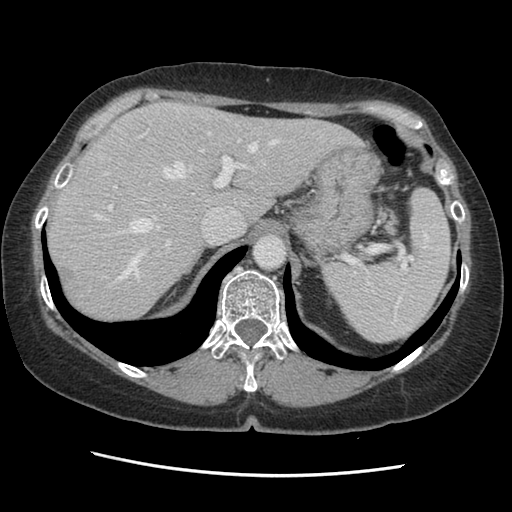
Contrast-enhanced abdominal CT, one axial slice; position 101 of 141 along the scan axis; soft-tissue window (W 400 / L 40 HU); 2.5 mm slice thickness; 512 × 512 image matrix, field of view 330 × 330 mm. Female patient, age 61 years. Case-level facts recorded for this patient, not image findings: diagnosis: colorectal cancer liver metastases, imaged before liver resection; multiple liver metastases: no; largest metastasis: 2.4 cm; chemotherapy before resection: no.
Structures marked on this image (manually delineated by an expert):
- hepatic veins: bounding box <94,117,278,282> (left, top, right, bottom; pixels)
- liver: <48,103,356,323>
- planned liver remnant (the part of the liver to remain after resection): <48,103,356,323>
- portal vein (with intrahepatic branches): <108,133,244,248>